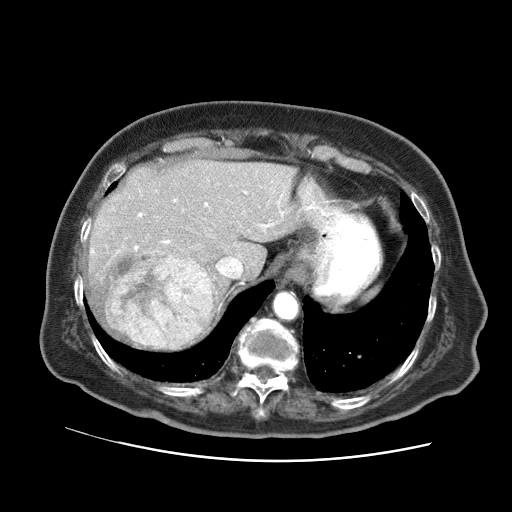
Contrast-enhanced abdominal CT (liver protocol), one axial slice. Position 52 of 73 along the scan axis. 120 kVp. Soft-tissue window (W 400 / L 40 HU). 2.5 mm slice thickness. 512 × 512 image matrix, field of view 380 × 380 mm. From the clinical record (not read from this slice): diagnosis: hepatocellular carcinoma (patient treated with transarterial chemoembolisation; whether this scan precedes or follows treatment is not stated here); TNM stage (as recorded): Stage-I; Child-Pugh class: A; tumour differentiation: well differentiated; tumour nodularity: uninodular.
Structures marked on this image (semi-automatically segmented with operator editing):
- liver parenchyma outside the tumour (the mass and vessels are separate outlines, so this box may not span the whole liver): bounding box (x1, y1, x2, y2) in pixels: (84, 160, 300, 351)
- mass: (104, 250, 213, 348)
- liver vessels: (91, 191, 284, 253)